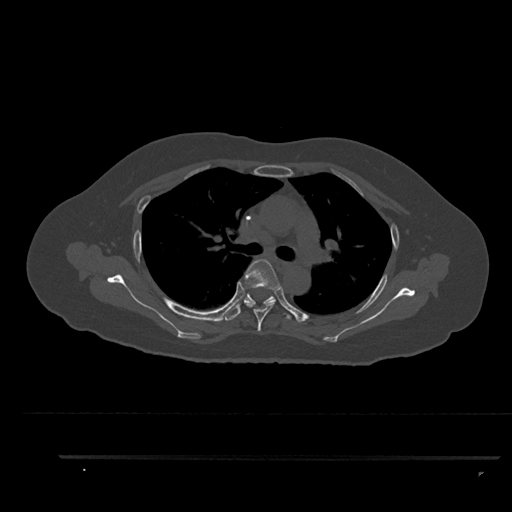
CT including the spine, one axial slice; position 624 of 797 along the scan axis; reconstruction kernel Br40s/3; 120 kVp; bone window (W 1800 / L 400 HU); 512 × 512 image matrix, field of view 408 × 408 mm. Patient: female, 44 years. From the clinical record (not read from this slice): primary cancer: renal.
Outlined on this slice (semi-automatically segmented with operator editing):
- T4 vertebra: bounding box [x1, y1, x2, y2] px = [244, 259, 281, 331]
- T5 vertebra: [225, 293, 291, 321]